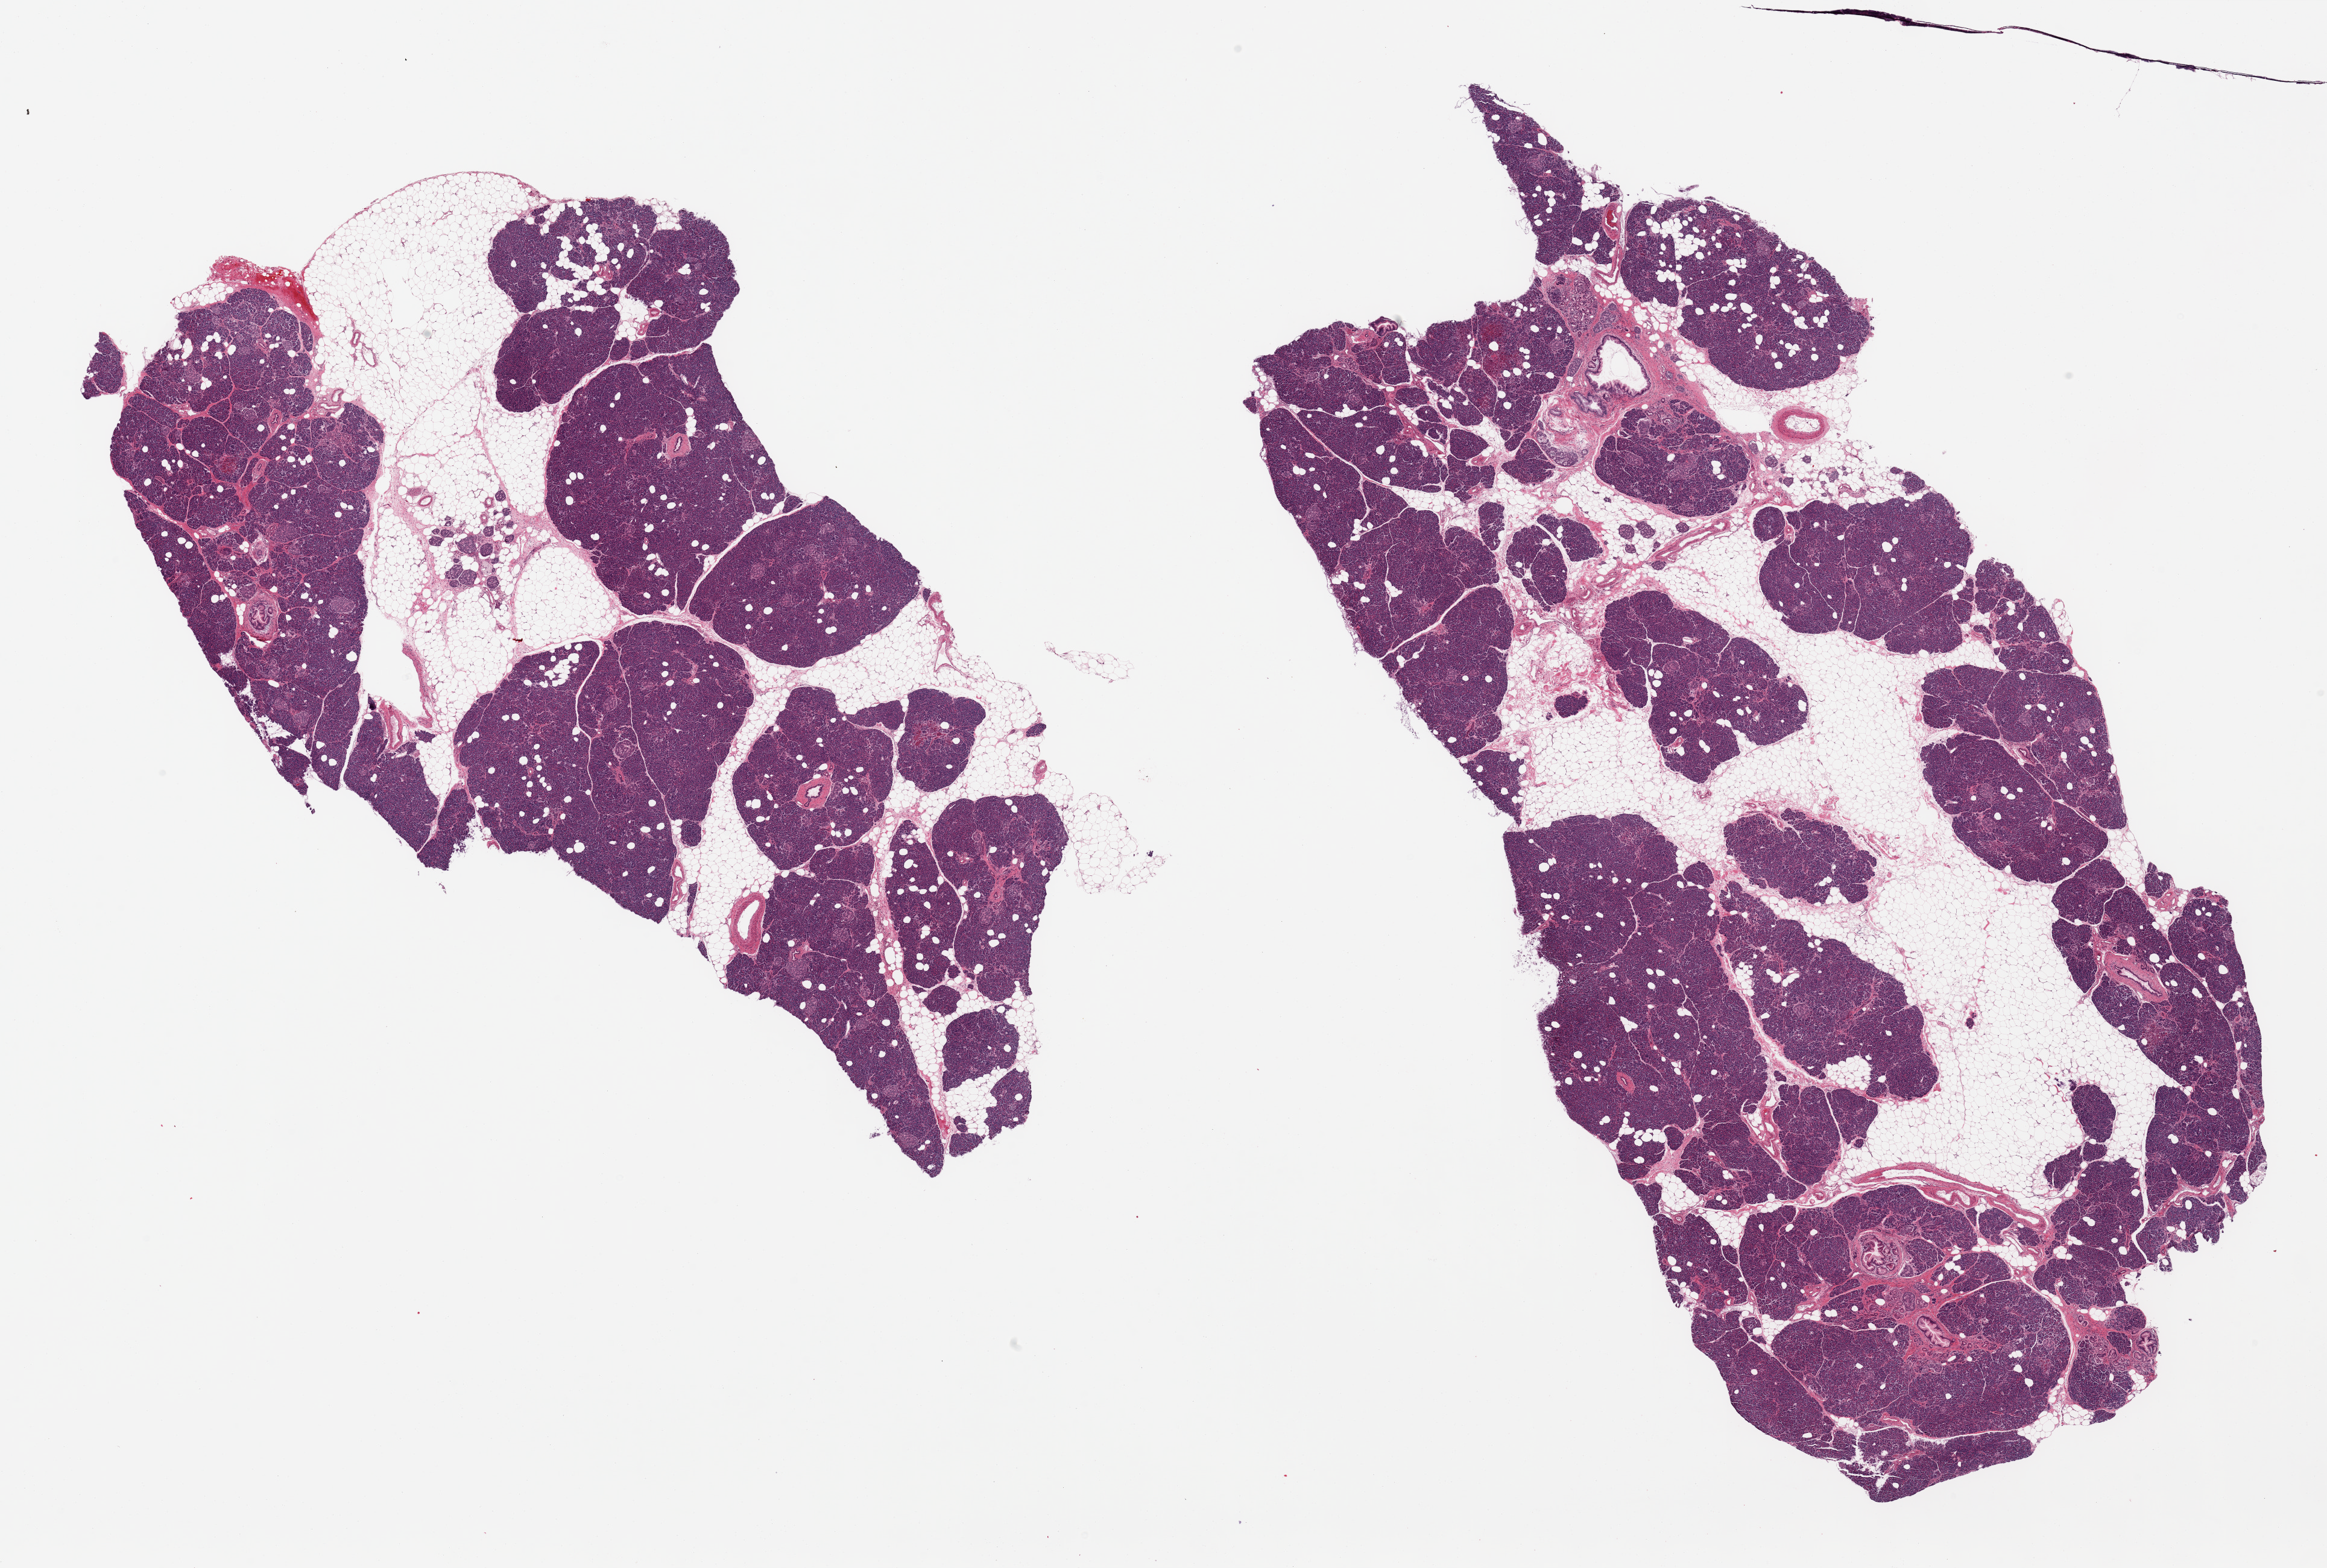
Digitized hematoxylin and eosin (H&E)-stained section, shown as a low-resolution overview of the whole scanned area (about 30.5 x 20.6 mm), PAXgene-fixed, paraffin-embedded tissue, sampled site (target tissue): pancreas, donor tissue sample.
Pathologist's review note for this sample: 2 pieces, Islets well preserved; Prominent mucinous ducts with mild proliferative changes suggestive of remote possible pancreatitis Interstitial fat is ~20% of tissue.